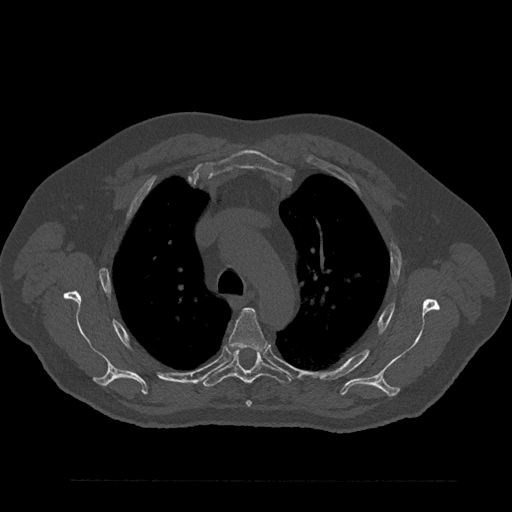
CT including the spine, one axial slice; slice 621 of 797 in the series (ordered by position); 120 kVp; bone window (W 1800 / L 400 HU); 512 × 512 image matrix. Male patient, age 61 years. Case-level facts recorded for this patient, not image findings: primary cancer: prostate.
Structures marked on this image (semi-automatically segmented with operator editing):
- T4 vertebra: bounding box (x1, y1, x2, y2) in pixels: (228, 307, 267, 407)
- T5 vertebra: (201, 349, 290, 387)